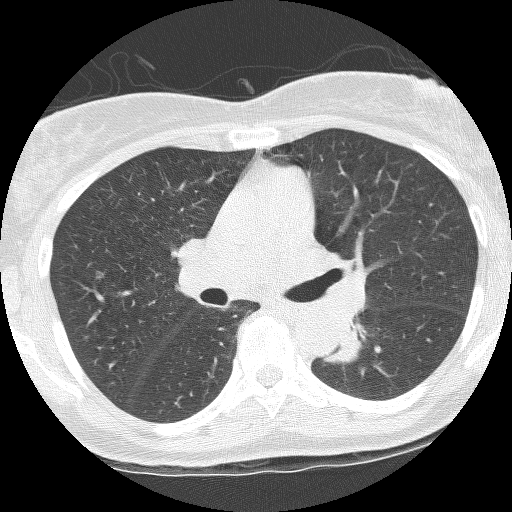
Chest CT (low-dose screening protocol), one axial image; third screening round (two years after baseline); lung window (W 1500 / L -600 HU); 2.5 mm slice thickness; lung (sharp) reconstruction kernel (BONE); 120 kVp; 512 × 512 image matrix, field of view 290 × 290 mm. Female, age 62 years at enrolment.
Lesion marked by an expert reader, box from (x=324, y=321) to (x=384, y=364) px. The screening reader recorded 3 non-calcified nodules or masses ≥4 mm on this exam; which of them this box marks is not recorded. Official screen result: positive, other. Later outcome: lung cancer diagnosed 165 days after this screen — squamous cell carcinoma, NOS, left lower lobe, stage IIIB (AJCC 6th edition), 31 mm at pathology.